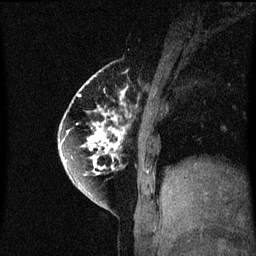
Breast MRI (dynamic contrast-enhanced), one sagittal slice; position 16 of 60 along the scan axis; dynamic contrast-enhanced series, image 2 of 3 at this slice position (ordered by acquisition); 1.5 T; TE 4.2 ms, TR 8.4 ms; 2 mm slice thickness; 256 × 256 image matrix, field of view 200 × 200 mm. Patient: female, 60 years.
Structures marked on this image (semi-automatic segmentation, software-assisted and operator-edited):
- analysis volume of interest (the breast-tissue region the enhancement analysis was run in; not a lesion): bounding box [x1, y1, x2, y2] px = [64, 70, 131, 195]
- tumour enhancement mask (voxels above the 70 % enhancement threshold inside the analysis volume of interest): [64, 76, 127, 177]